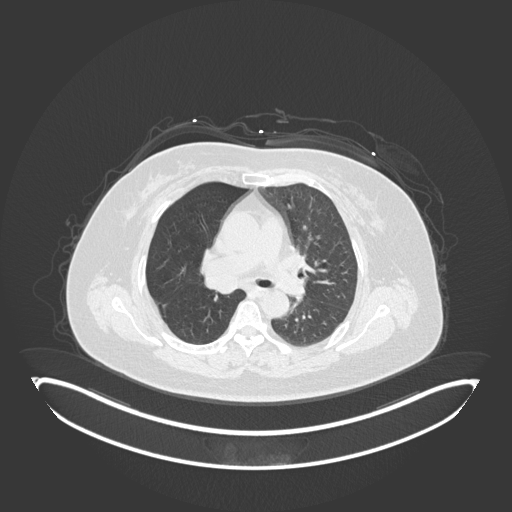
Chest CT, one axial slice. Position 101 of 245 along the scan axis. Reconstruction kernel B30f. 120 kVp. Lung window (W 1500 / L -600 HU). 512 × 512 image matrix, field of view 500 × 500 mm. Female patient, age 60 years. Case-level facts recorded for this patient, not image findings: clinical TNM (as recorded): T1c N0 M0.
Structures marked on this image (bounding box drawn by a radiologist):
- lung tumour (recorded histology: squamous cell carcinoma): bounding box (x1, y1, x2, y2) in pixels: (204, 271, 242, 293)